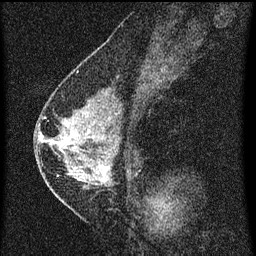
Breast MRI (dynamic contrast-enhanced), one sagittal slice. Slice 29 of 60 in the series (ordered by position). Dynamic contrast-enhanced series, image 2 of 3 at this slice position (ordered by acquisition). 1.5 T. TE 4.2 ms, TR 8 ms. 256 × 256 image matrix. Patient: female, 47 years.
Structures marked on this image (semi-automatic segmentation, software-assisted and operator-edited):
- analysis volume of interest (the breast-tissue region the enhancement analysis was run in; not a lesion): bounding box [x1, y1, x2, y2] px = [42, 92, 140, 199]
- tumour enhancement mask (voxels above the 70 % enhancement threshold inside the analysis volume of interest): [42, 122, 109, 177]